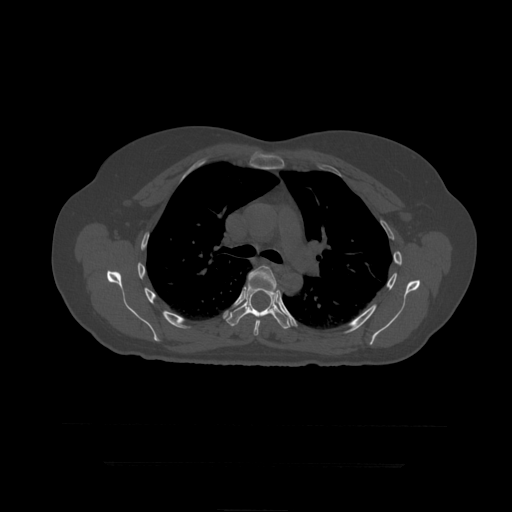
CT including the spine, one axial slice; 120 kVp; bone window (W 1800 / L 400 HU); 512 × 512 image matrix. Patient age 41 years. Case-level facts recorded for this patient, not image findings: primary cancer: breast.
Annotated regions visible in this slice (semi-automatic segmentation, software-assisted and operator-edited):
- T6 vertebra: bounding box <248,266,277,336> (left, top, right, bottom; pixels)
- T7 vertebra: <225,276,292,330>